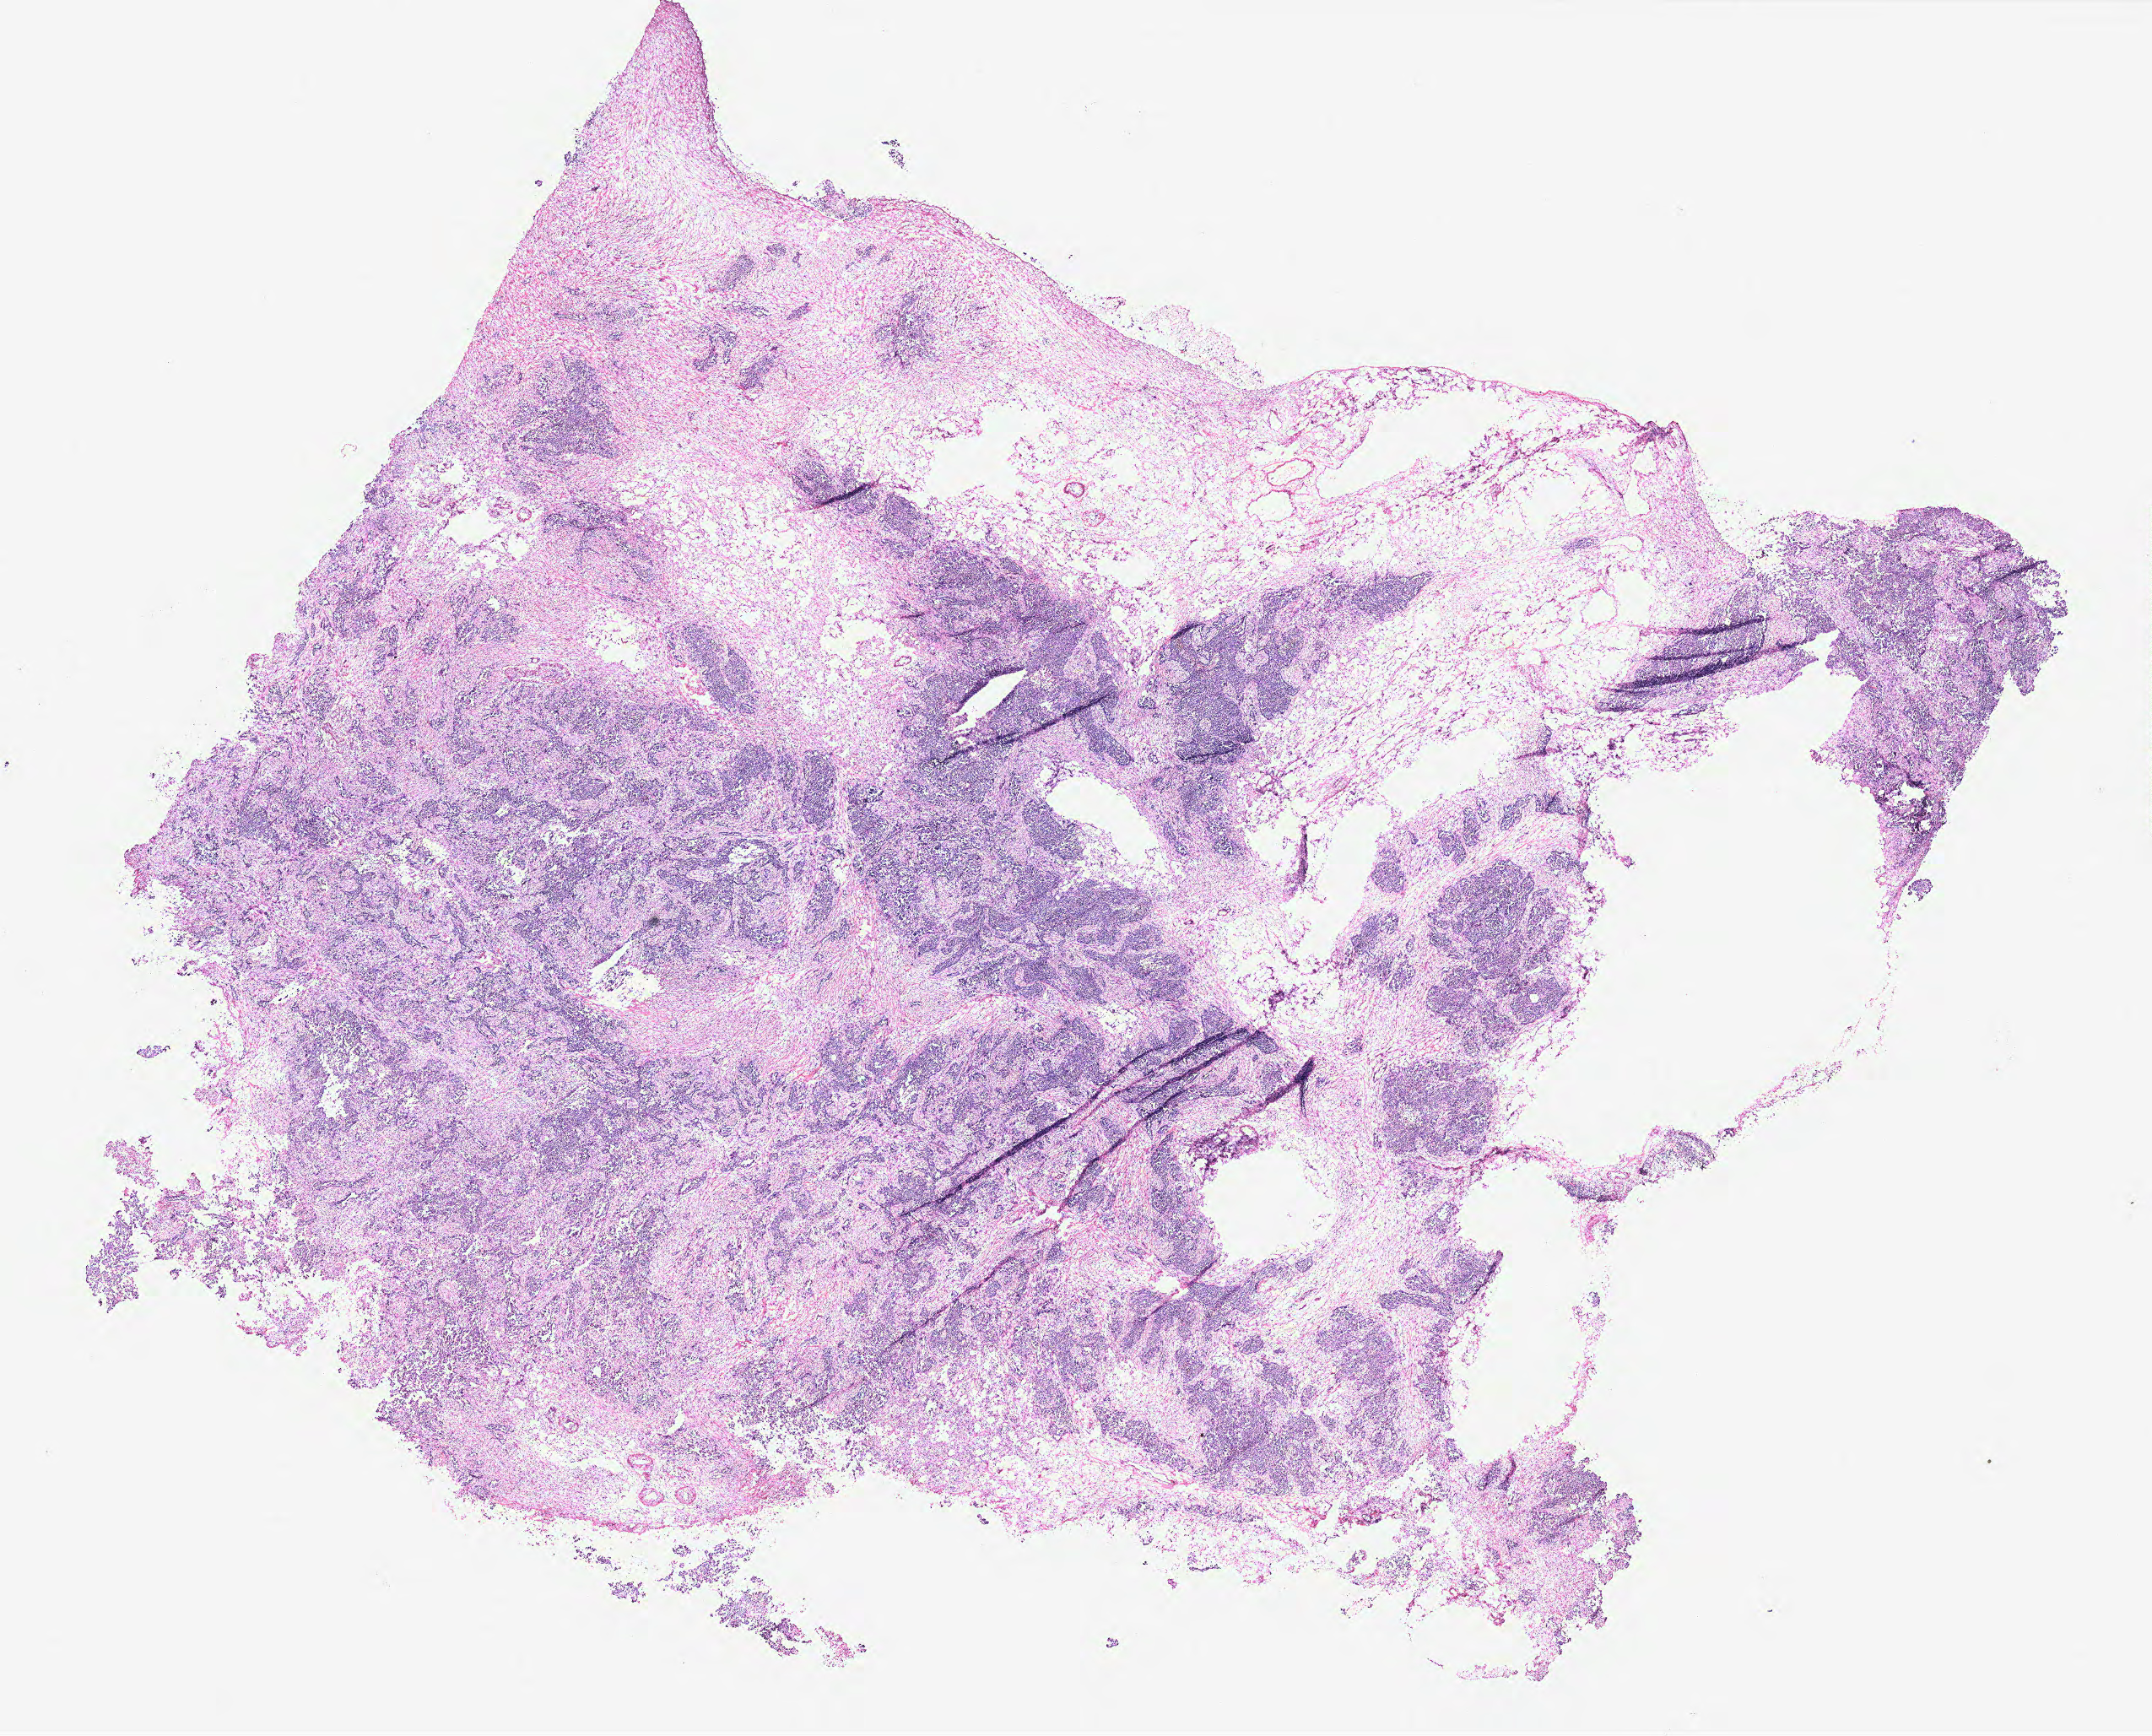
Digitized H&E-stained tissue section (whole slide), whole scanned area (about 20.4 x 16.5 mm, from a 40x scan) shown as a low-resolution overview. Tumour tissue sample, ovary. 62-year-old female patient.
Diagnosis: Serous adenocarcinoma, NOS.